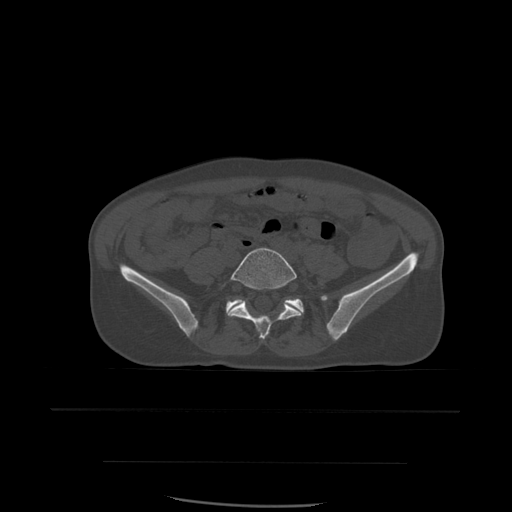
CT including the spine, one axial slice. Position 143 of 574 along the scan axis. Bone window (W 1800 / L 400 HU). 1.25 mm slice thickness. 512 × 512 image matrix, field of view 392 × 392 mm. Patient age 48 years. Case-level facts recorded for this patient, not image findings: primary cancer: lung.
Annotated regions visible in this slice (semi-automatically segmented with operator editing):
- L5 vertebra: bounding box [x1, y1, x2, y2] px = [223, 248, 304, 340]